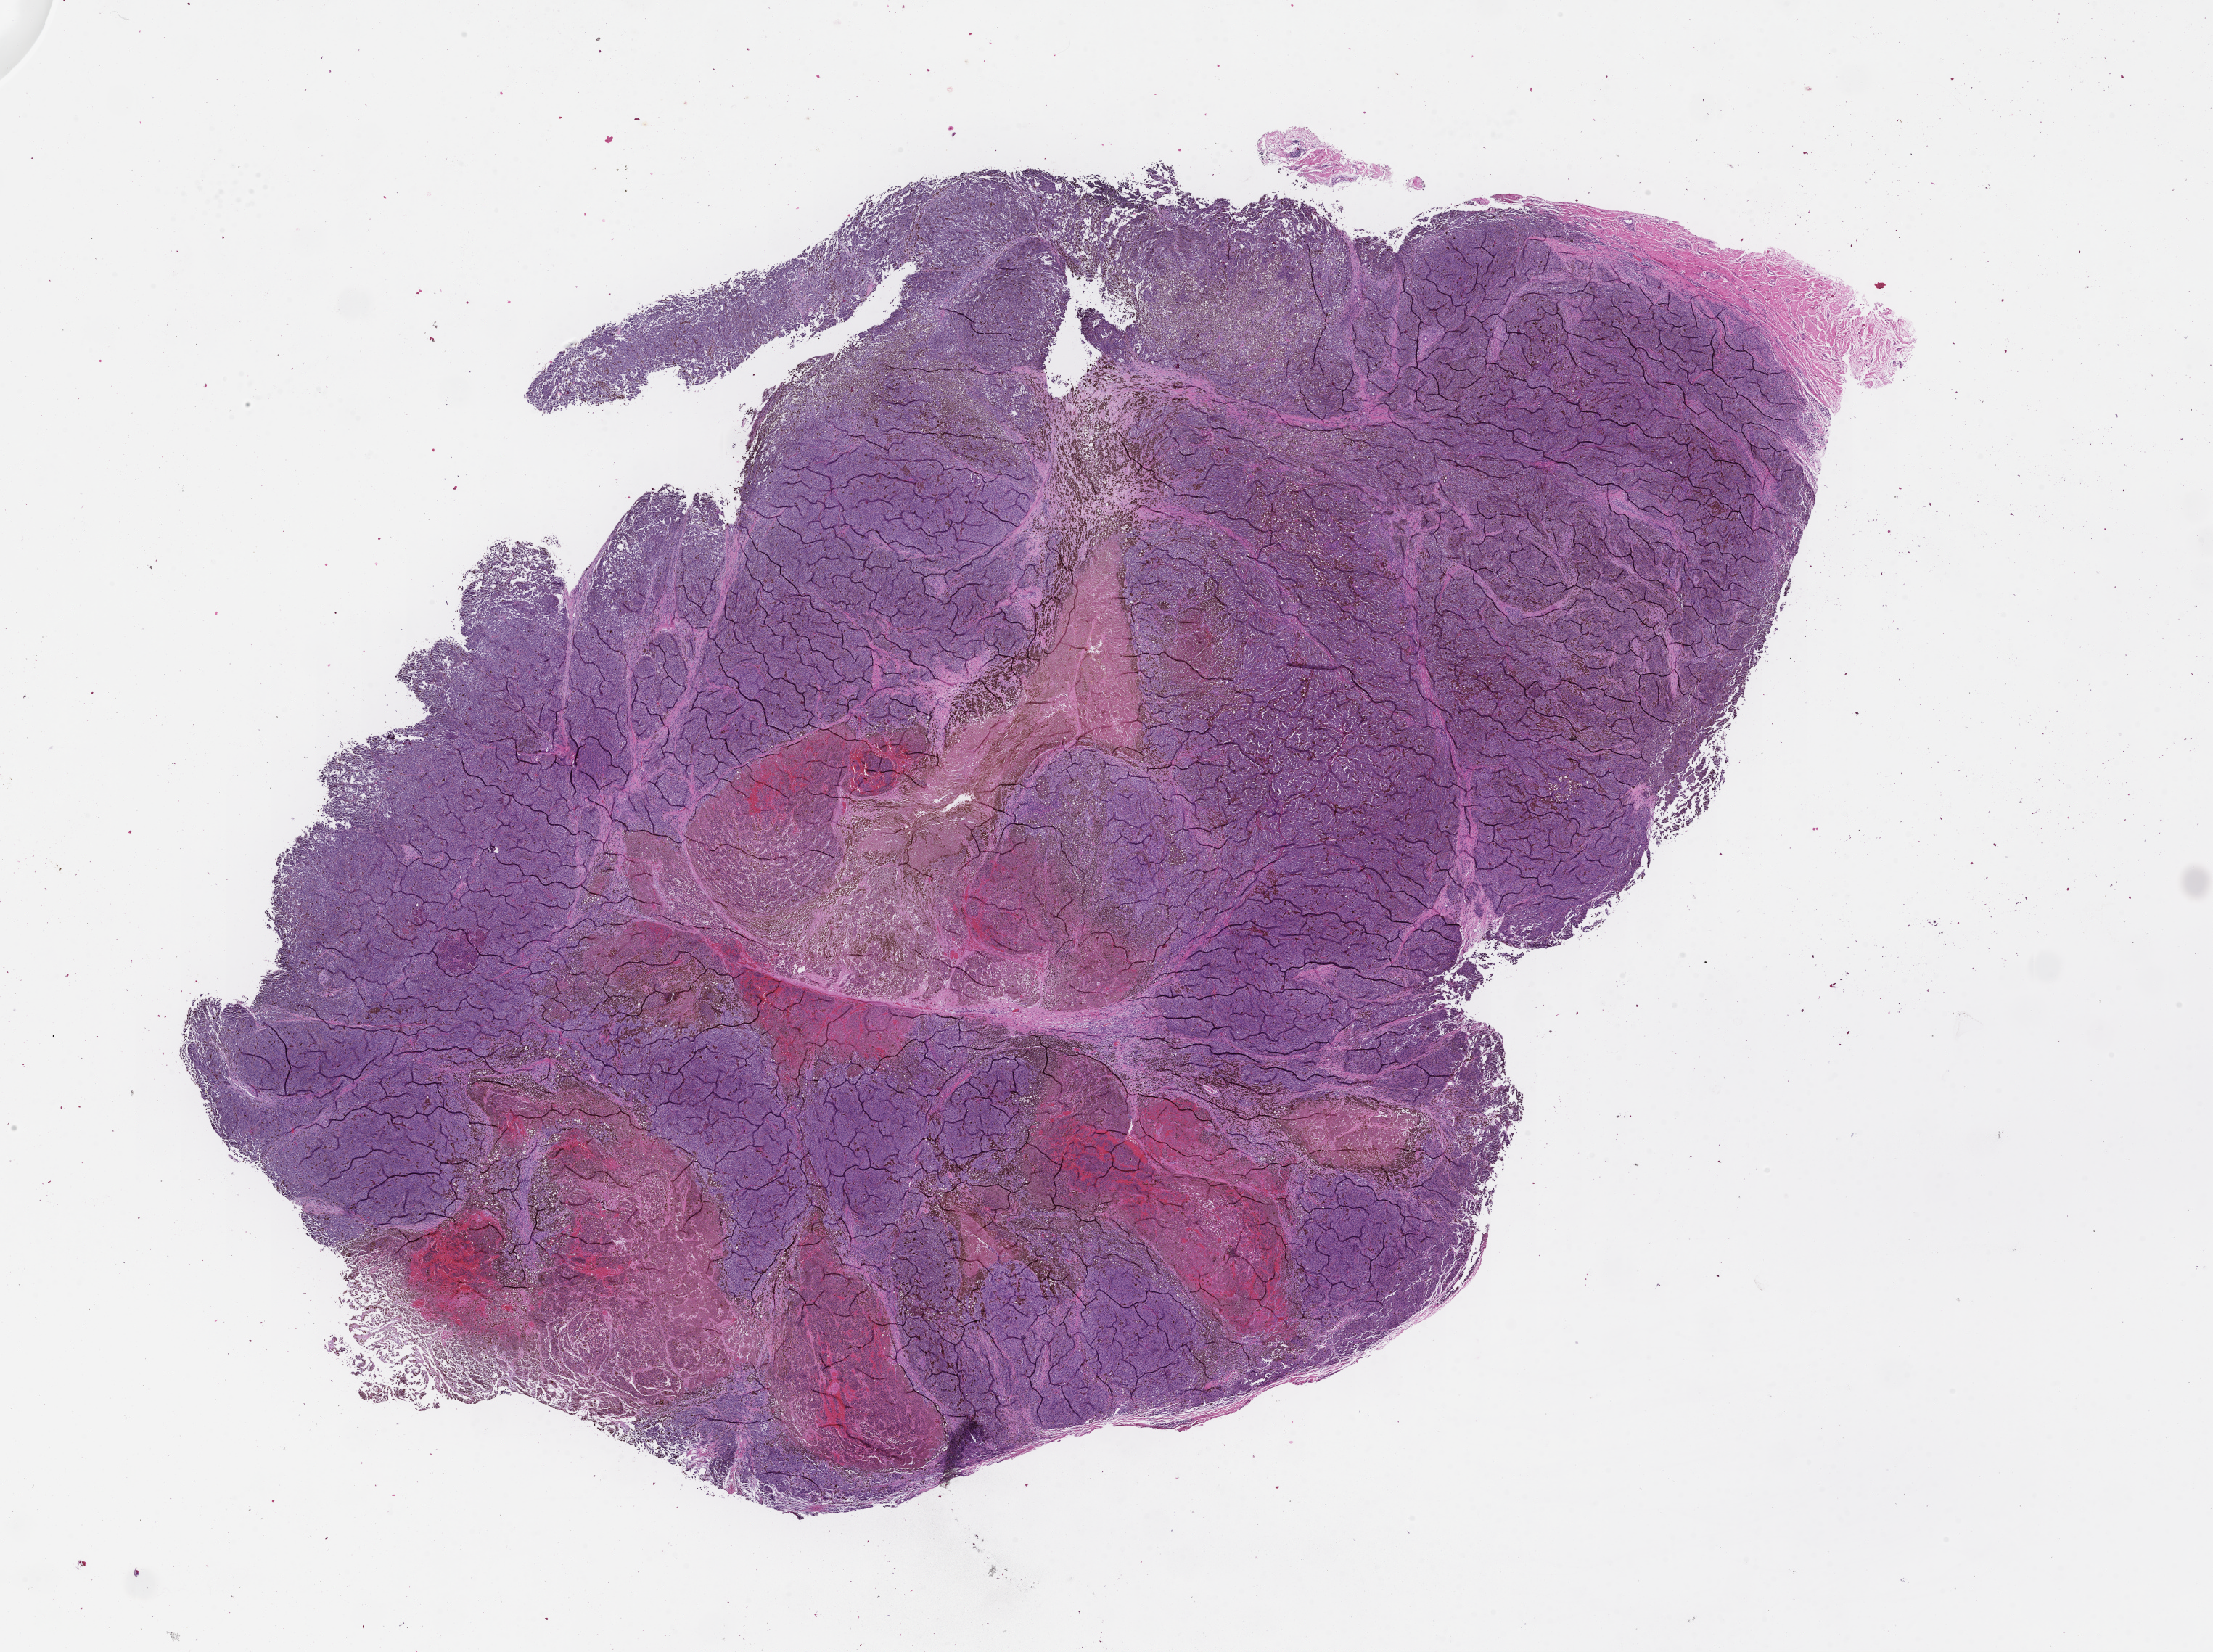
Whole-slide image, hematoxylin and eosin (H&E) stain, low-resolution overview of the scanned area, about 24.6 x 18.4 mm. FFPE section. Tissue site: skin. Collected at baseline (before treatment). Male patient.
From a patient with: Melanoma.